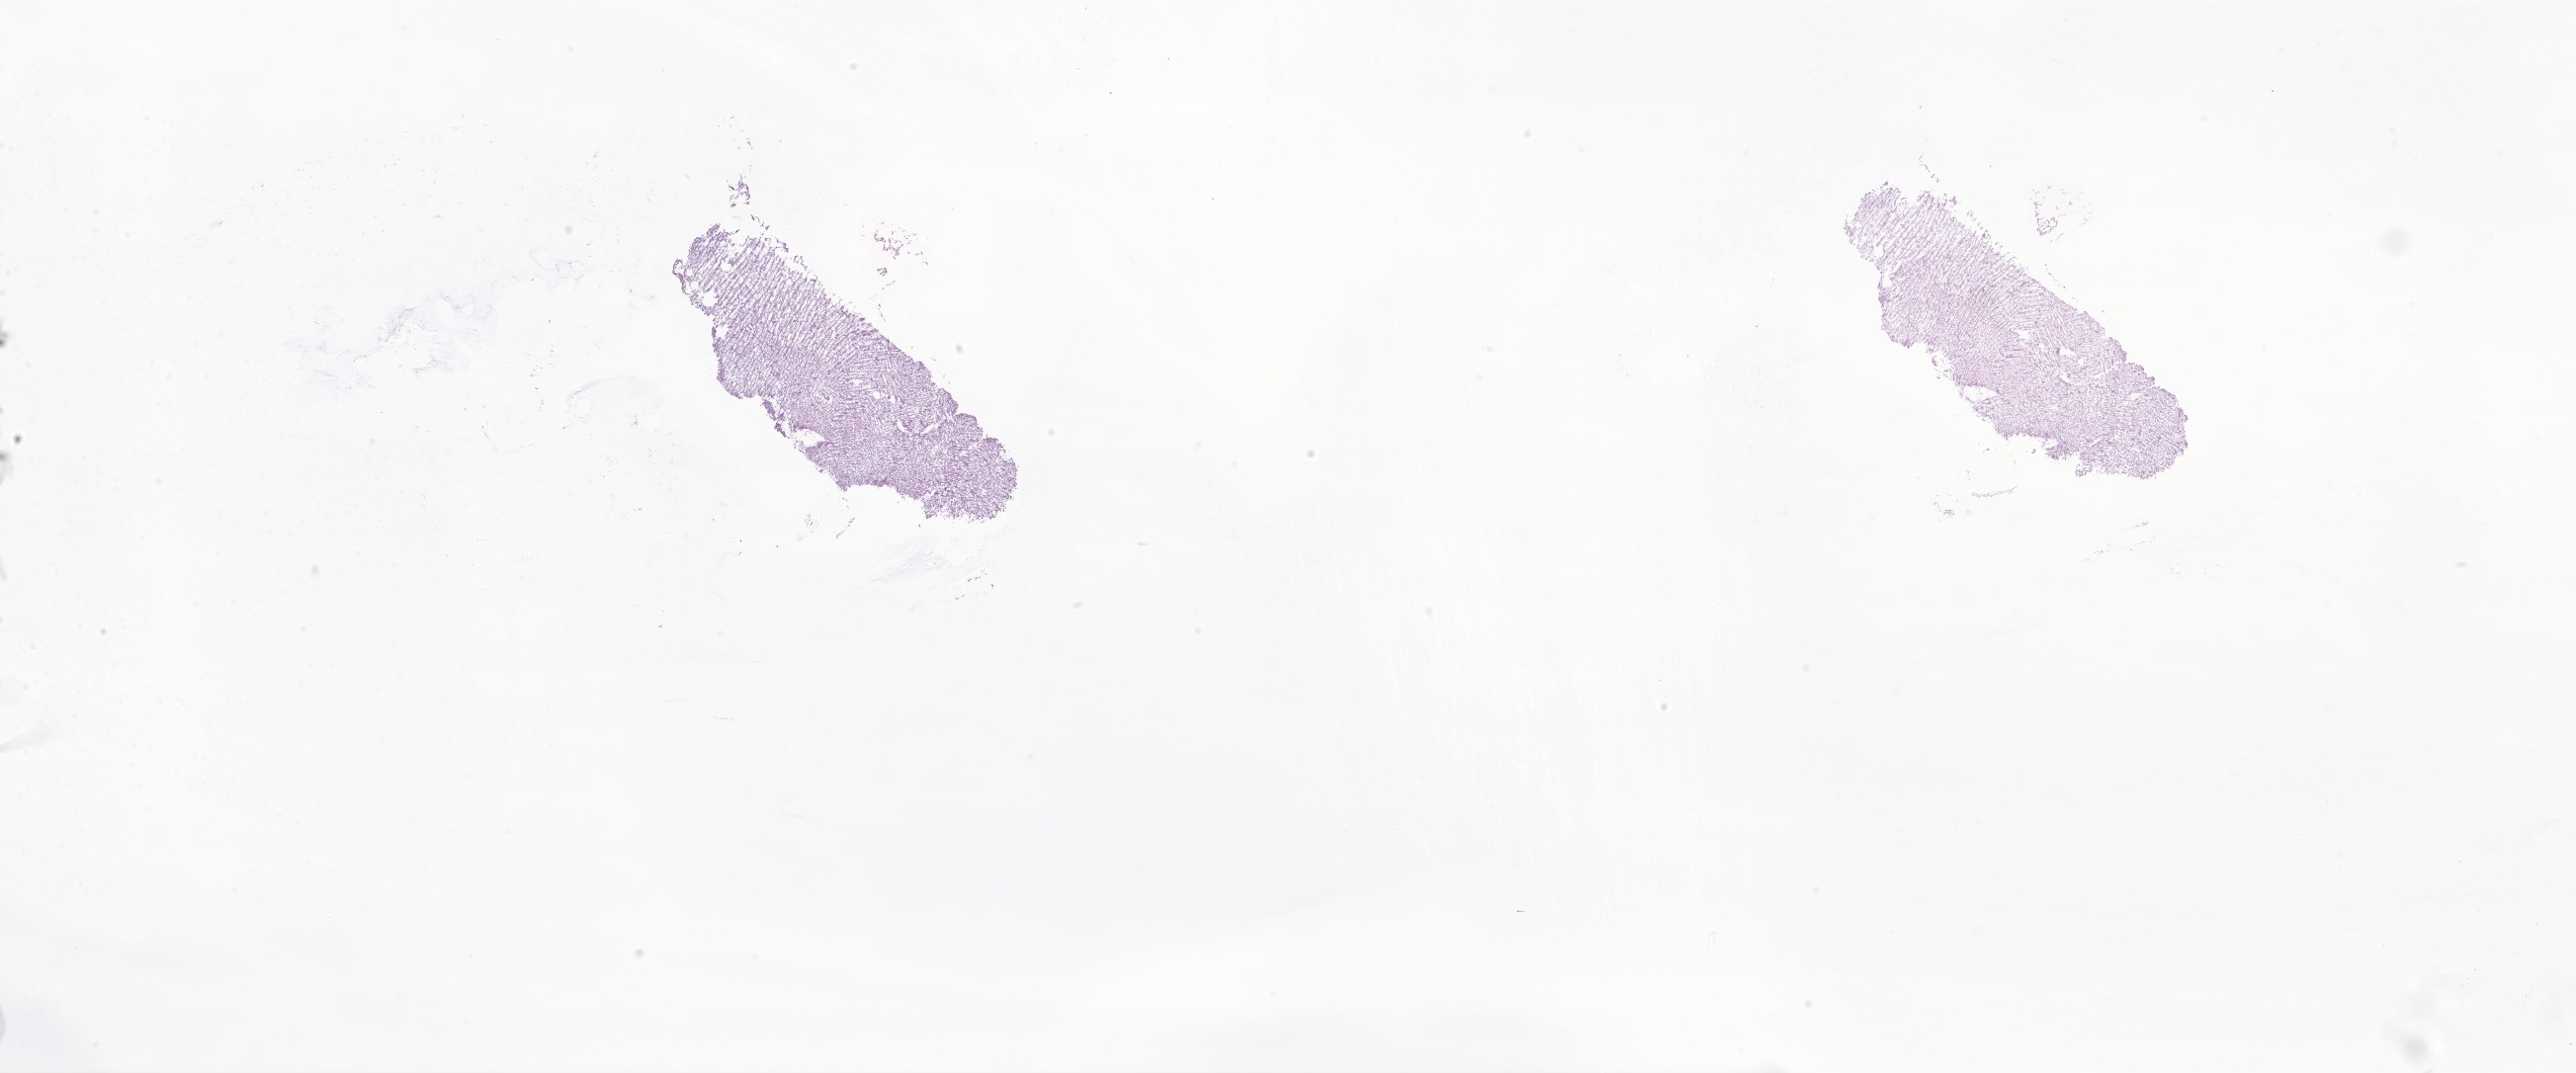
Digitized hematoxylin and eosin (H&E)-stained section of tumor tissue from the brain — a low-resolution overview of the entire scanned area, about 44.0 x 18.3 mm. Frozen section. Patient male; age 199 months (16 years 7 months).
- recorded diagnosis: Ganglioglioma, NOS